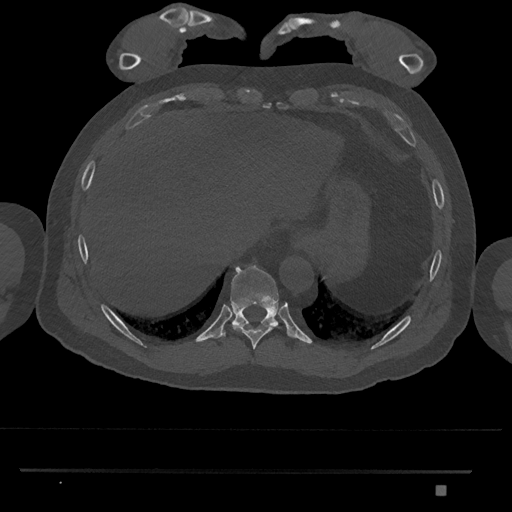
CT including the spine, one axial slice; position 1028 of 1134 along the scan axis; 120 kVp; bone window (W 1800 / L 400 HU); 512 × 512 image matrix, field of view 429 × 429 mm. Male patient, age 65 years. Case-level facts recorded for this patient, not image findings: primary cancer: prostate.
Structures marked on this image (semi-automatically segmented with operator editing):
- T10 vertebra: box from (x=221, y=264) to (x=279, y=339) px
- T9 vertebra: (x=232, y=324)–(x=279, y=350)